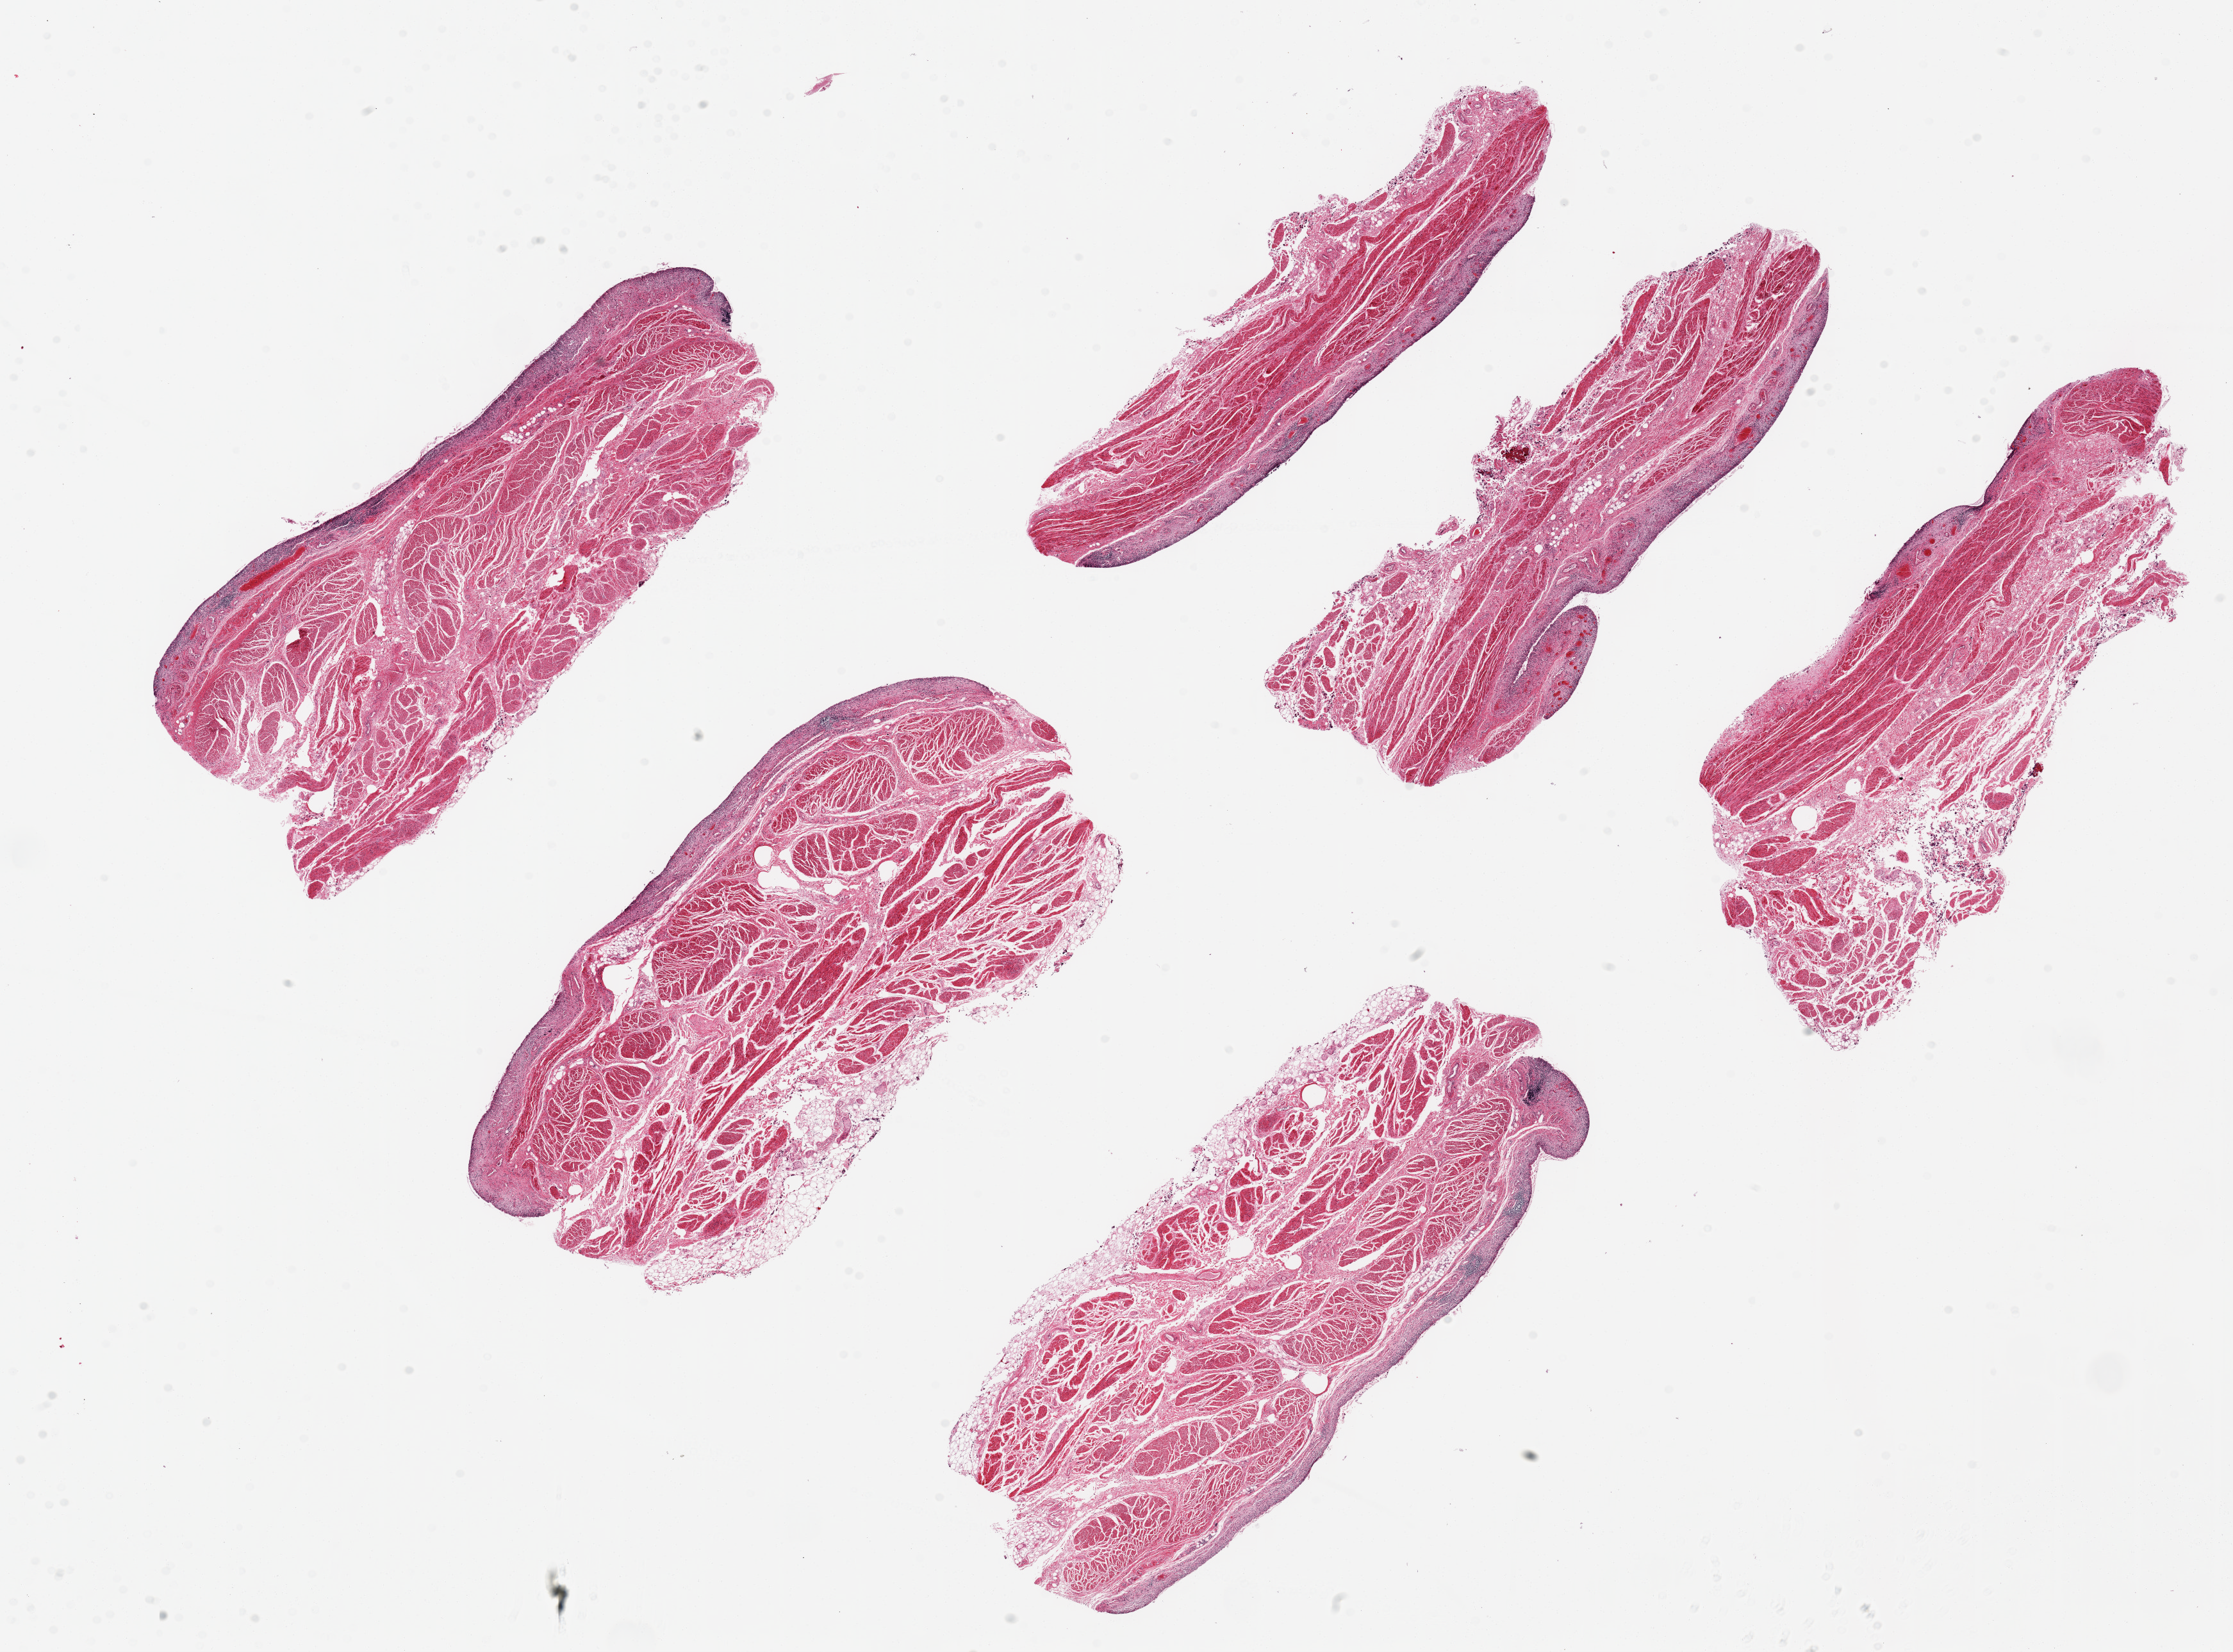
Whole-slide image, haematoxylin and eosin stain, a low-resolution overview of the entire scanned area, about 27.6 x 20.4 mm (from a 20x scan); PAXgene-fixed paraffin-embedded (PFPE) section; target tissue: urinary bladder; tissue donor sample. Donor: female.
• review note (as recorded): 6 ~ 8.5x3mmpieces, urothelium nearly totally sloughed, where present badly autolyzed; evidence of extensive chronic cystitis, uncertain etiology